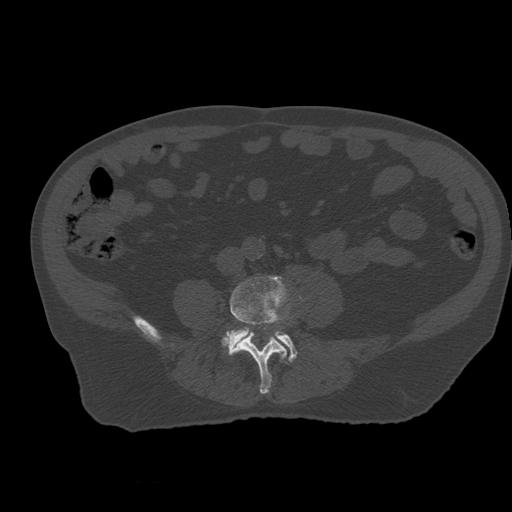
CT including the spine, one axial slice; 120 kVp; bone window (W 1800 / L 400 HU); 512 × 512 image matrix, field of view 407 × 407 mm. Patient age 73 years. From the clinical record (not read from this slice): primary cancer: prostate.
Outlined on this slice (semi-automatically segmented with operator editing):
- L4 vertebra: box from (x=221, y=276) to (x=291, y=394) px
- L5 vertebra: (x=228, y=327)–(x=298, y=362)